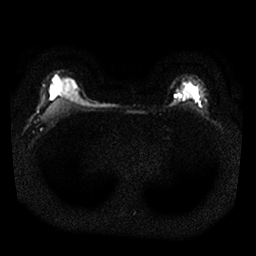
Breast MRI, one axial slice; slice 23 of 25 in the series (ordered by position); diffusion-weighted series; image 2 of 4 stored at this slice position (different b-values; order by instance number); 1.5 T; 4 mm slice thickness; 256 × 256 image matrix. Female patient.
Structures marked on this image (manually delineated by an expert):
- tumour on diffusion-weighted imaging: box from (x=182, y=97) to (x=185, y=100) px